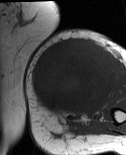
MRI of an extremity soft-tissue mass, one axial slice; MR volume resampled by the dataset authors to the PET/CT grid (not the native acquisition matrix); 3.27 mm slice thickness; 126 × 155 image matrix, field of view 123 × 151 mm. Female patient. Case-level facts recorded for this patient, not image findings: histological type: pleiomorphic leiomyosarcoma; grade: high; site of the primary tumour: left biceps.
Outlined on this slice (expert contour drawn on MRI and transferred to this co-registered scan by the dataset authors):
- gross tumour volume including surrounding oedema: bounding box <31,40,115,118> (left, top, right, bottom; pixels)
- gross tumour volume (mass): <31,40,115,118>